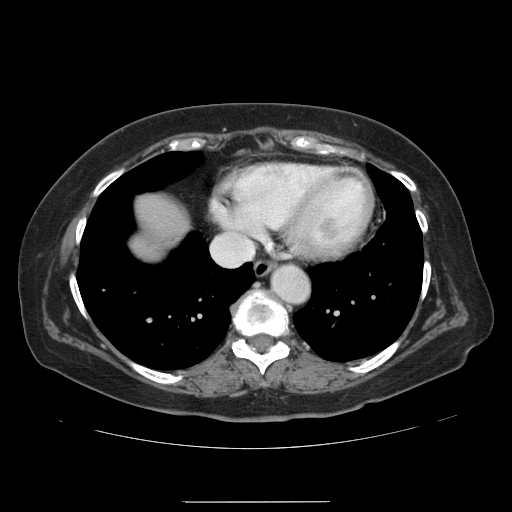
Contrast-enhanced abdominal CT, one axial slice; slice 129 of 141 in the series (ordered by position); intravenous contrast given; soft-tissue window (W 400 / L 40 HU); 2.5 mm slice thickness; 512 × 512 image matrix. Female patient, age 74 years. From the clinical record (not read from this slice): diagnosis: colorectal cancer liver metastases, imaged before liver resection; multiple liver metastases: yes; largest metastasis: 7 cm; chemotherapy before resection: no.
Annotated regions visible in this slice (outlined manually by an expert reader):
- liver: bounding box (x1, y1, x2, y2) in pixels: (133, 198, 185, 255)
- planned liver remnant (the part of the liver to remain after resection): (137, 198, 173, 254)